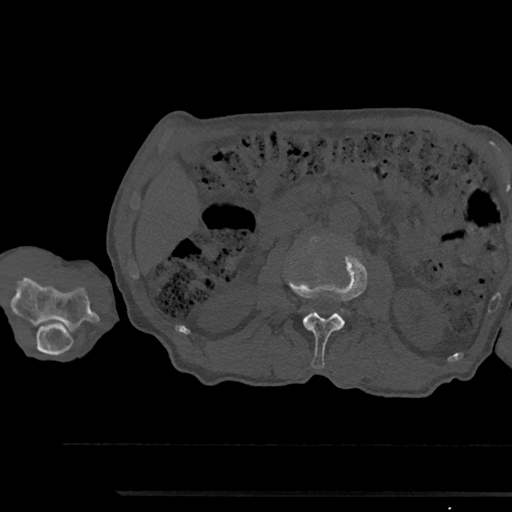
CT including the spine, one axial slice; slice 546 of 797 in the series (ordered by position); 120 kVp; bone window (W 1800 / L 400 HU); 0.5 mm slice thickness; 512 × 512 image matrix, field of view 367 × 367 mm. Patient: male, 79 years. From the clinical record (not read from this slice): primary cancer: prostate.
Annotated regions visible in this slice (semi-automatic segmentation, software-assisted and operator-edited):
- L2 vertebra: bounding box <289,246,367,368> (left, top, right, bottom; pixels)